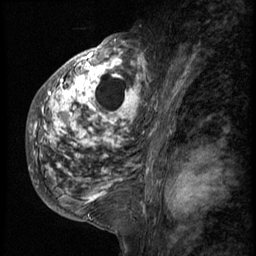
Breast MRI (dynamic contrast-enhanced), one sagittal slice; position 32 of 58 along the scan axis; 3 images stored at this slice position (order not interpretable as contrast timing); 1.5 T; TE 4.2 ms, TR 9 ms; 2.5 mm slice thickness; 256 × 256 image matrix, field of view 180 × 180 mm. Female patient, age 50 years. From the clinical record (not read from this slice): setting: breast cancer imaged before/during neoadjuvant chemotherapy; receptor status: triple-negative.
Annotated regions visible in this slice (semi-automatically segmented with operator editing):
- analysis volume of interest (the breast-tissue region the enhancement analysis was run in; not a lesion): box from (x=27, y=48) to (x=147, y=214) px
- tumour enhancement mask (voxels above the 140 % enhancement threshold inside the analysis volume of interest): (x=30, y=48)–(x=147, y=203)